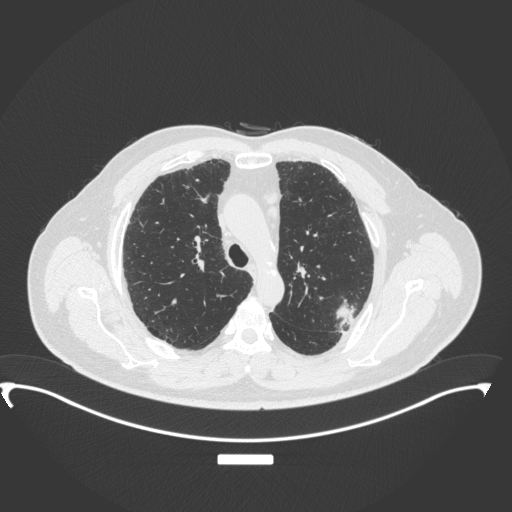
Chest CT, one axial slice; slice 257 of 350 in the series (ordered by position); reconstruction kernel B31f; 120 kVp; lung window (W 1500 / L -600 HU); 512 × 512 image matrix, field of view 459 × 459 mm. Patient: male, 64 years. Case-level facts recorded for this patient, not image findings: clinical TNM (as recorded): T1c N1 M1.
Outlined on this slice (bounding box drawn by a radiologist):
- lung tumour (recorded histology: adenocarcinoma): bounding box [x1, y1, x2, y2] px = [328, 297, 364, 335]